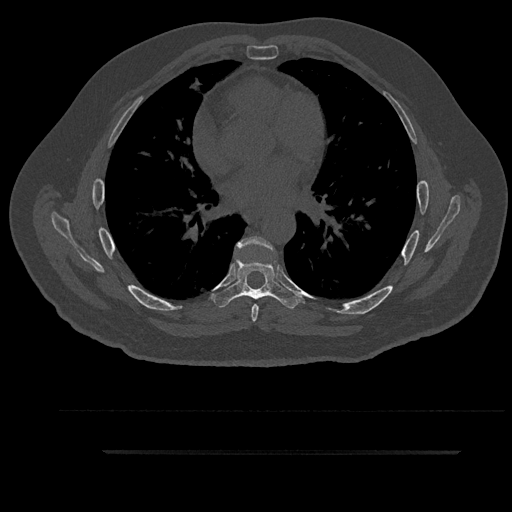
CT including the spine, one axial slice. Slice 545 of 797 in the series (ordered by position). Reconstruction kernel Br40s/3. Bone window (W 1800 / L 400 HU). 0.5 mm slice thickness. 512 × 512 image matrix. Male patient, age 63 years. From the clinical record (not read from this slice): primary cancer: renal; vertebrae with lytic lesions (as recorded): T8.
Annotated regions visible in this slice (semi-automatic segmentation, software-assisted and operator-edited):
- T6 vertebra: bounding box (x1, y1, x2, y2) in pixels: (236, 236, 273, 322)
- T7 vertebra: (212, 258, 299, 309)